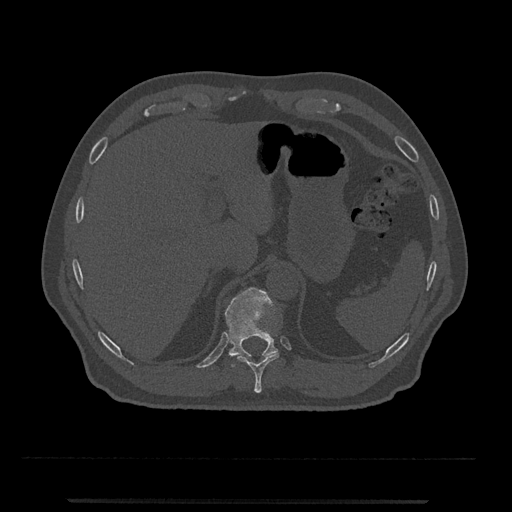
CT including the spine, one axial slice. Slice 490 of 797 in the series (ordered by position). Reconstruction kernel Br40s/3. 120 kVp. Bone window (W 1800 / L 400 HU). 512 × 512 image matrix, field of view 419 × 419 mm. Patient: male, 63 years. Case-level facts recorded for this patient, not image findings: primary cancer: prostate.
Annotated regions visible in this slice (semi-automatically segmented with operator editing):
- T10 vertebra: box from (x=237, y=352) to (x=280, y=393) px
- T11 vertebra: (x=225, y=287)–(x=278, y=367)